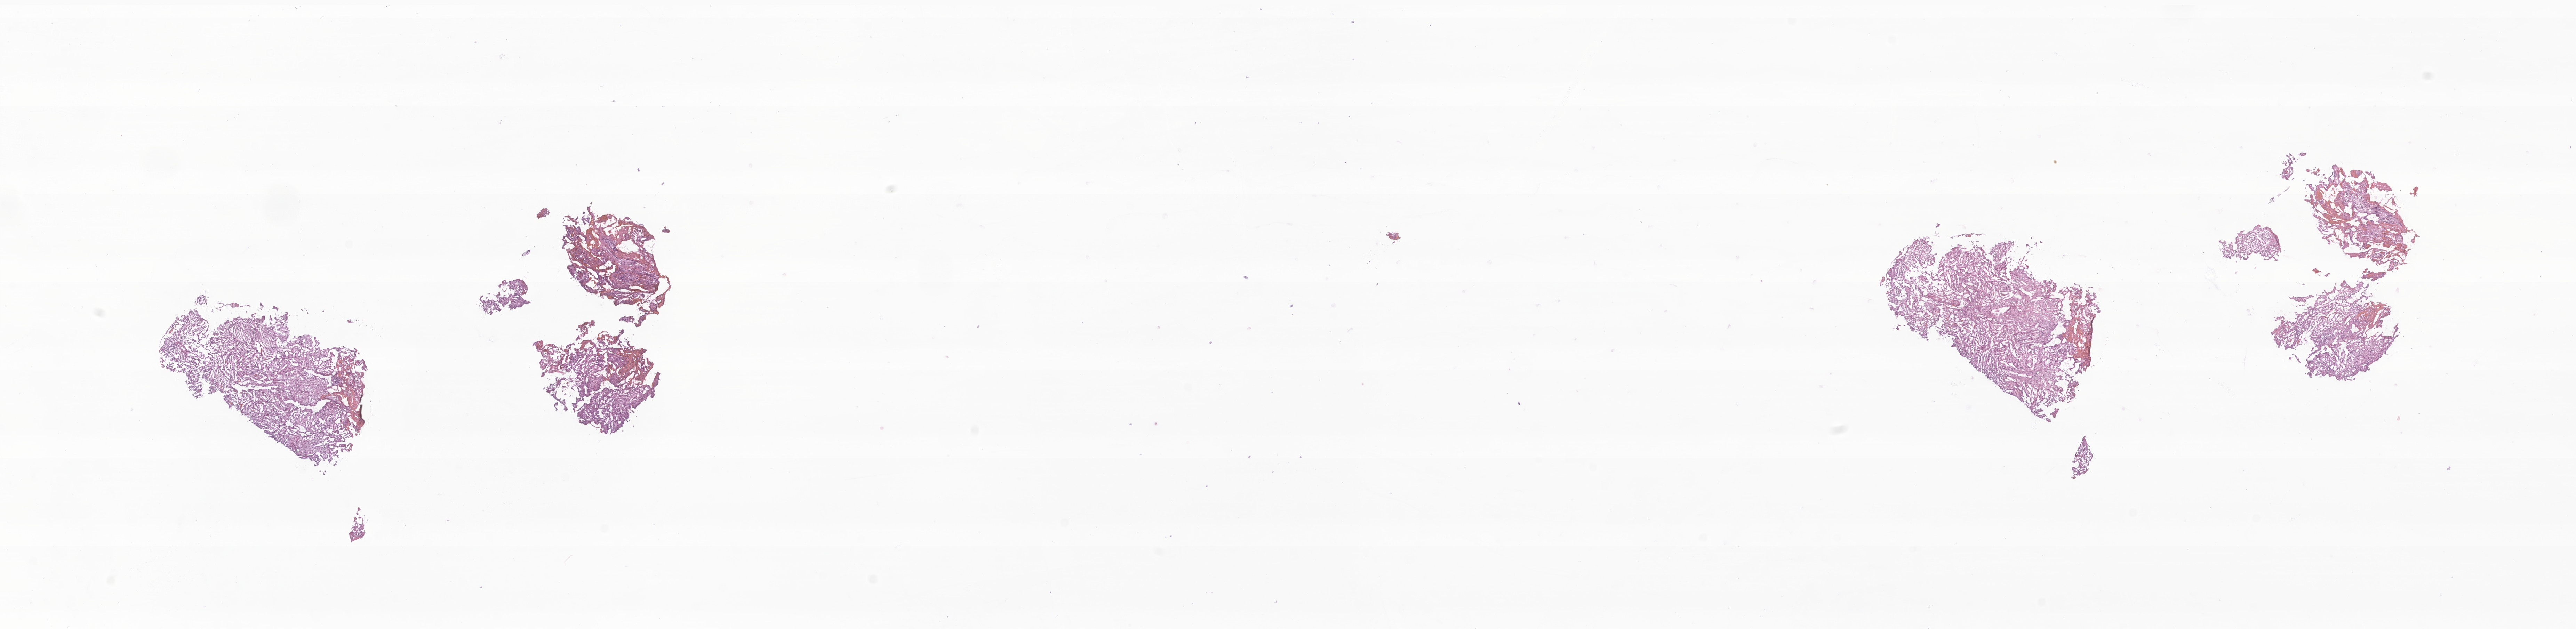
Haematoxylin and eosin whole-slide image of tumor tissue from the temporal lobe — a low-resolution overview of the entire scanned area, about 31.2 x 7.6 mm; cryosection (OCT / tissue freezing medium). Male patient, age 820 days.
Diagnosis: Pleomorphic xanthoastrocytoma, NOS.